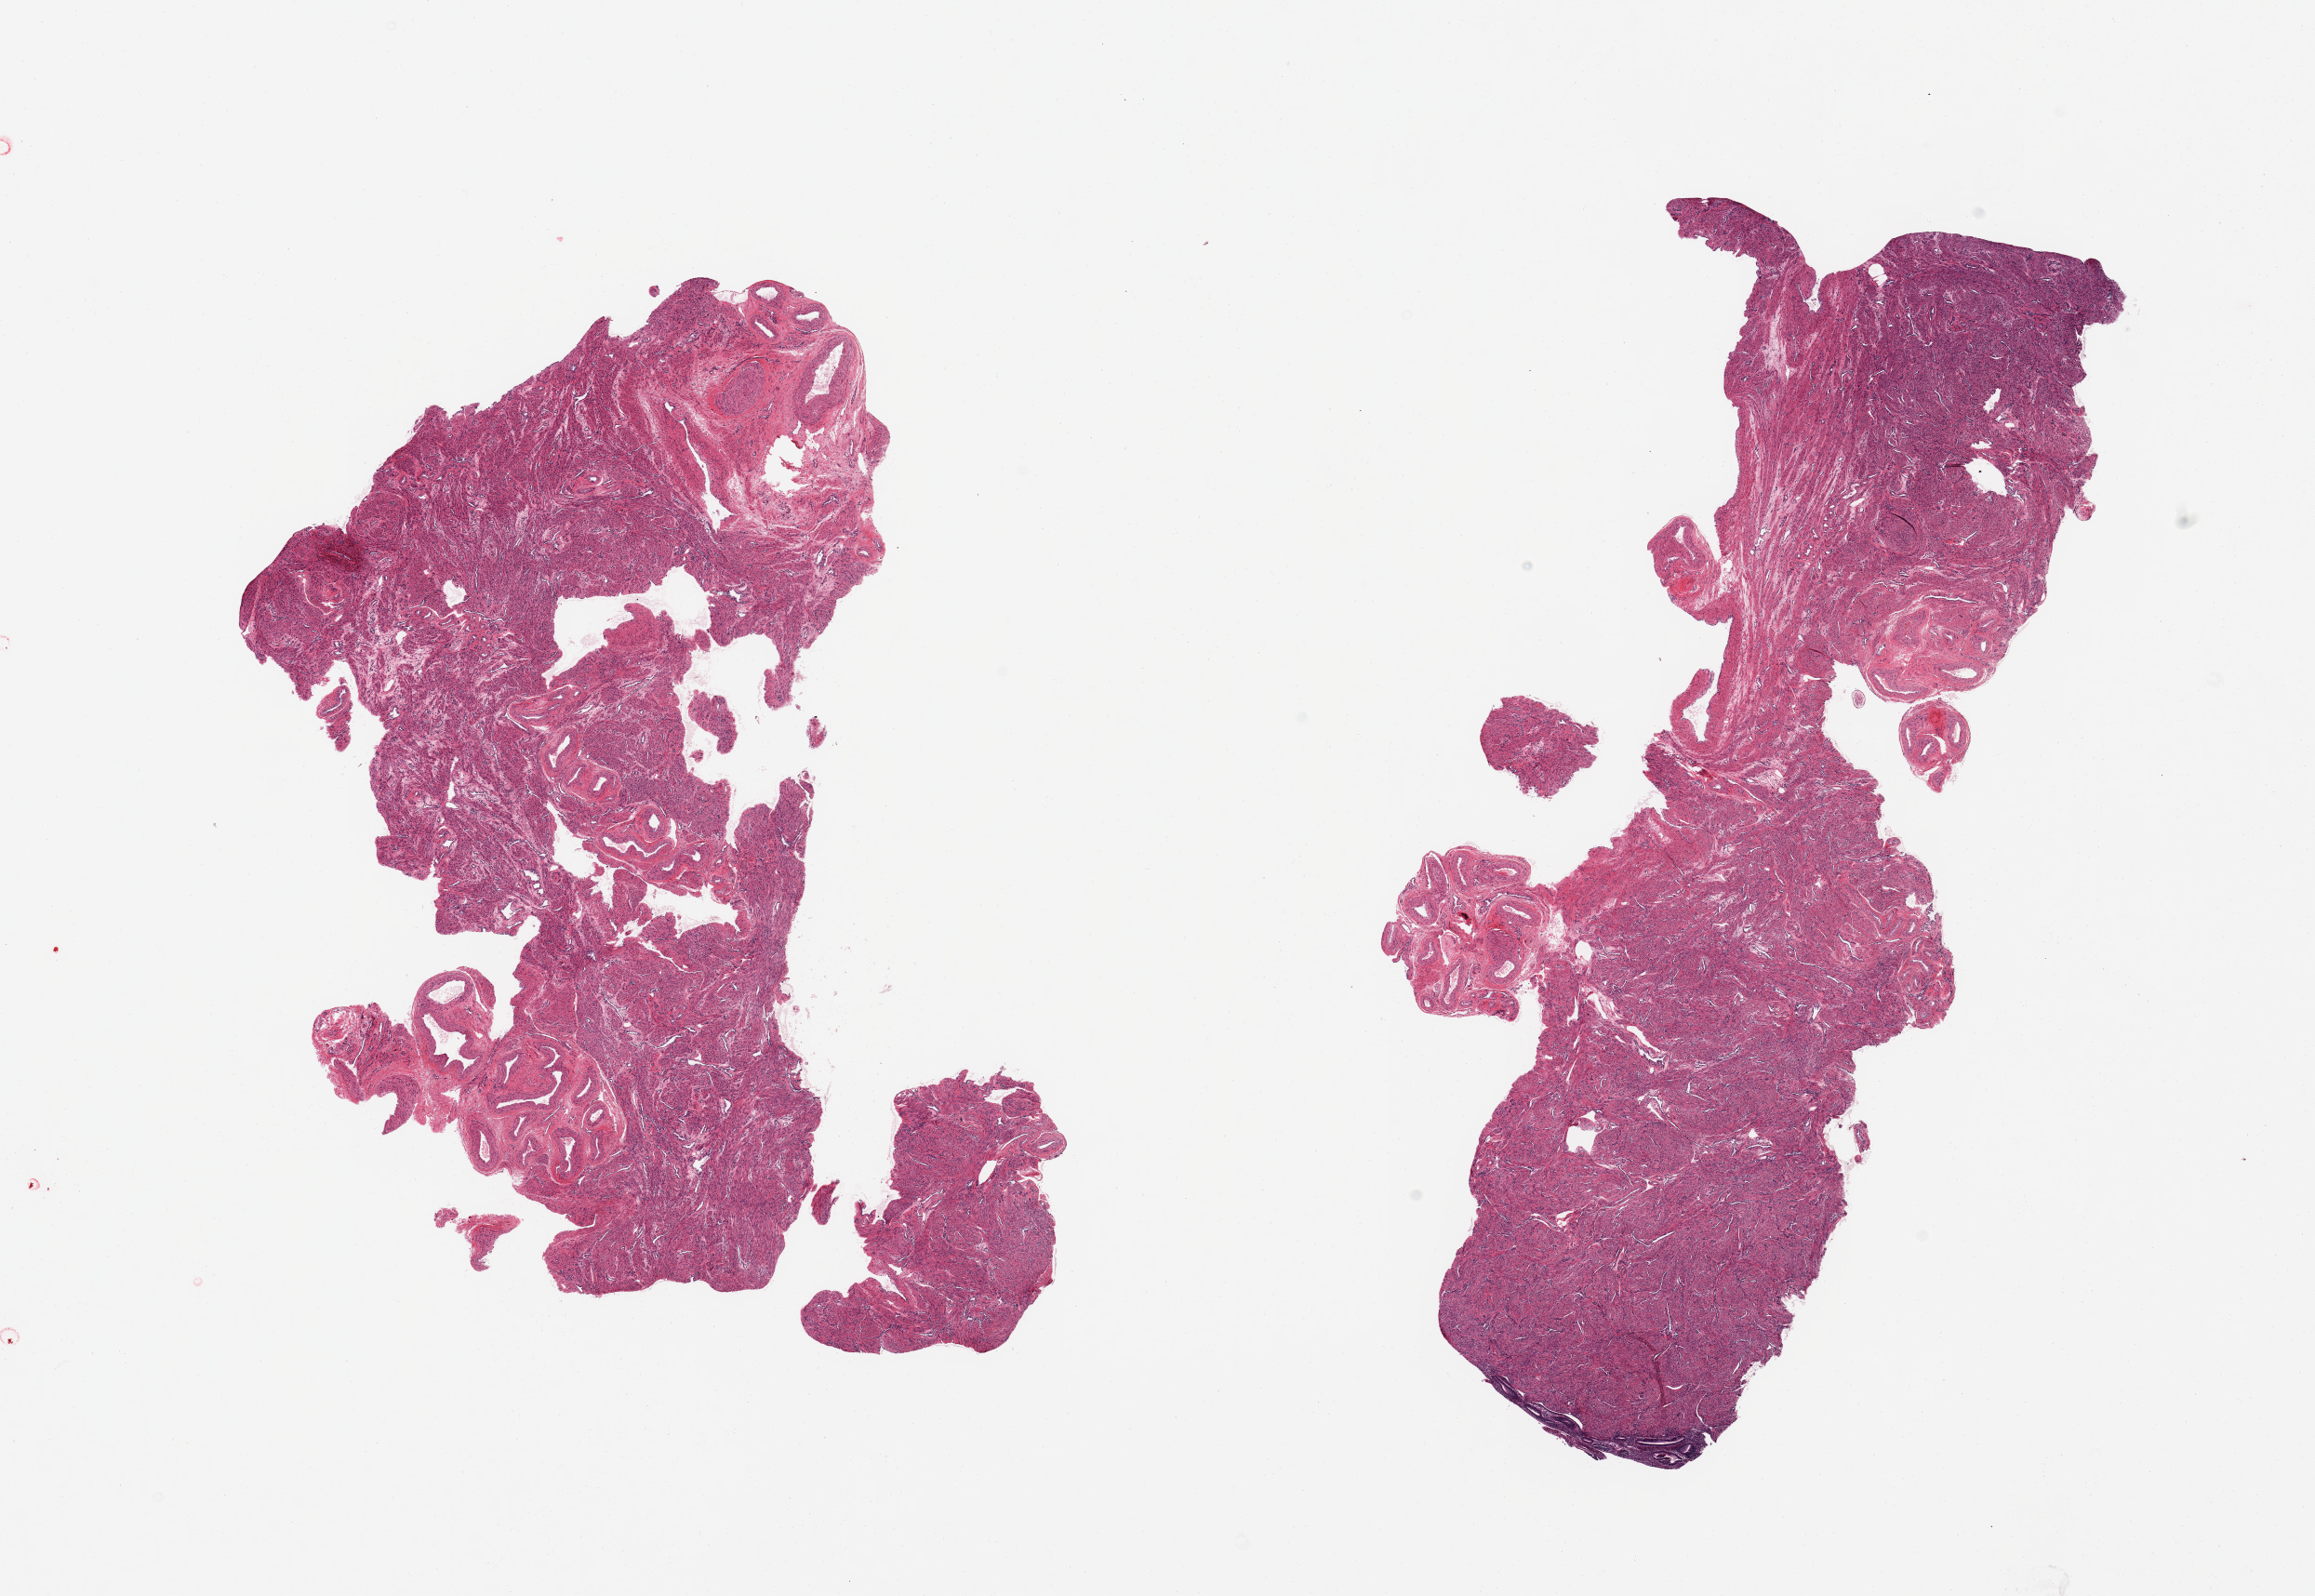
Hematoxylin and eosin (H&E) whole-slide image, brightfield — a low-resolution overview of the entire scanned area, about 19.7 x 13.6 mm. PAXgene-fixed paraffin-embedded (PFPE) section. Sampled site (target tissue): uterus. Donor tissue sample. Donor sex: female.
• review note (as recorded): 2 pieces, principally myometrium; trace inactive/basalis endometrium, ~0.2mm noted